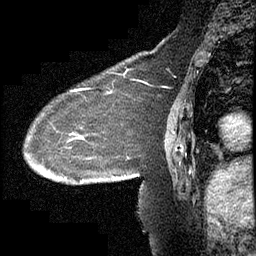
Breast MRI (dynamic contrast-enhanced), one sagittal slice; slice 145 of 232 in the series (ordered by position); dynamic contrast-enhanced study with each time point stored as its own series, time point 2 of 4 at this slice position (early post-contrast, ordered by acquisition time); 1.5 T; TE 4.2 ms, TR 6.7 ms; 3 mm slice thickness; 256 × 256 image matrix, field of view 200 × 200 mm. Female patient, age 63 years. Case-level facts recorded for this patient, not image findings: setting: breast cancer imaged before/during neoadjuvant chemotherapy; receptor status: triple-negative.
Outlined on this slice (semi-automatically segmented with operator editing):
- analysis volume of interest (the breast-tissue region the enhancement analysis was run in; not a lesion): bounding box [x1, y1, x2, y2] px = [24, 90, 140, 211]
- tumour enhancement mask (voxels above the 70 % enhancement threshold inside the analysis volume of interest): [73, 90, 115, 179]